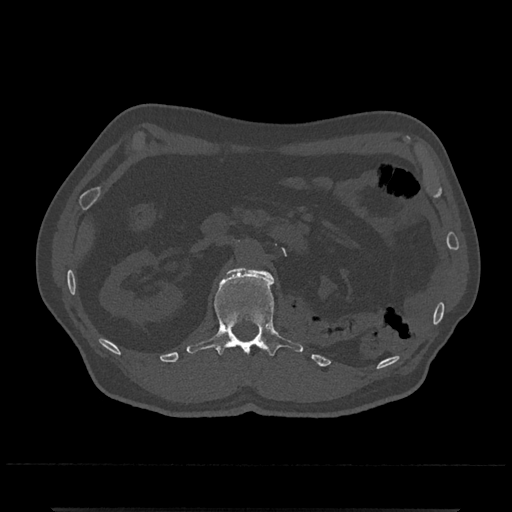
CT including the spine, one axial slice. Slice 361 of 797 in the series (ordered by position). 120 kVp. Bone window (W 1800 / L 400 HU). 512 × 512 image matrix, field of view 393 × 393 mm. Patient: male, 67 years. Case-level facts recorded for this patient, not image findings: primary cancer: prostate.
Annotated regions visible in this slice (semi-automatic segmentation, software-assisted and operator-edited):
- L1 vertebra: box from (x=186, y=267) to (x=303, y=356) px